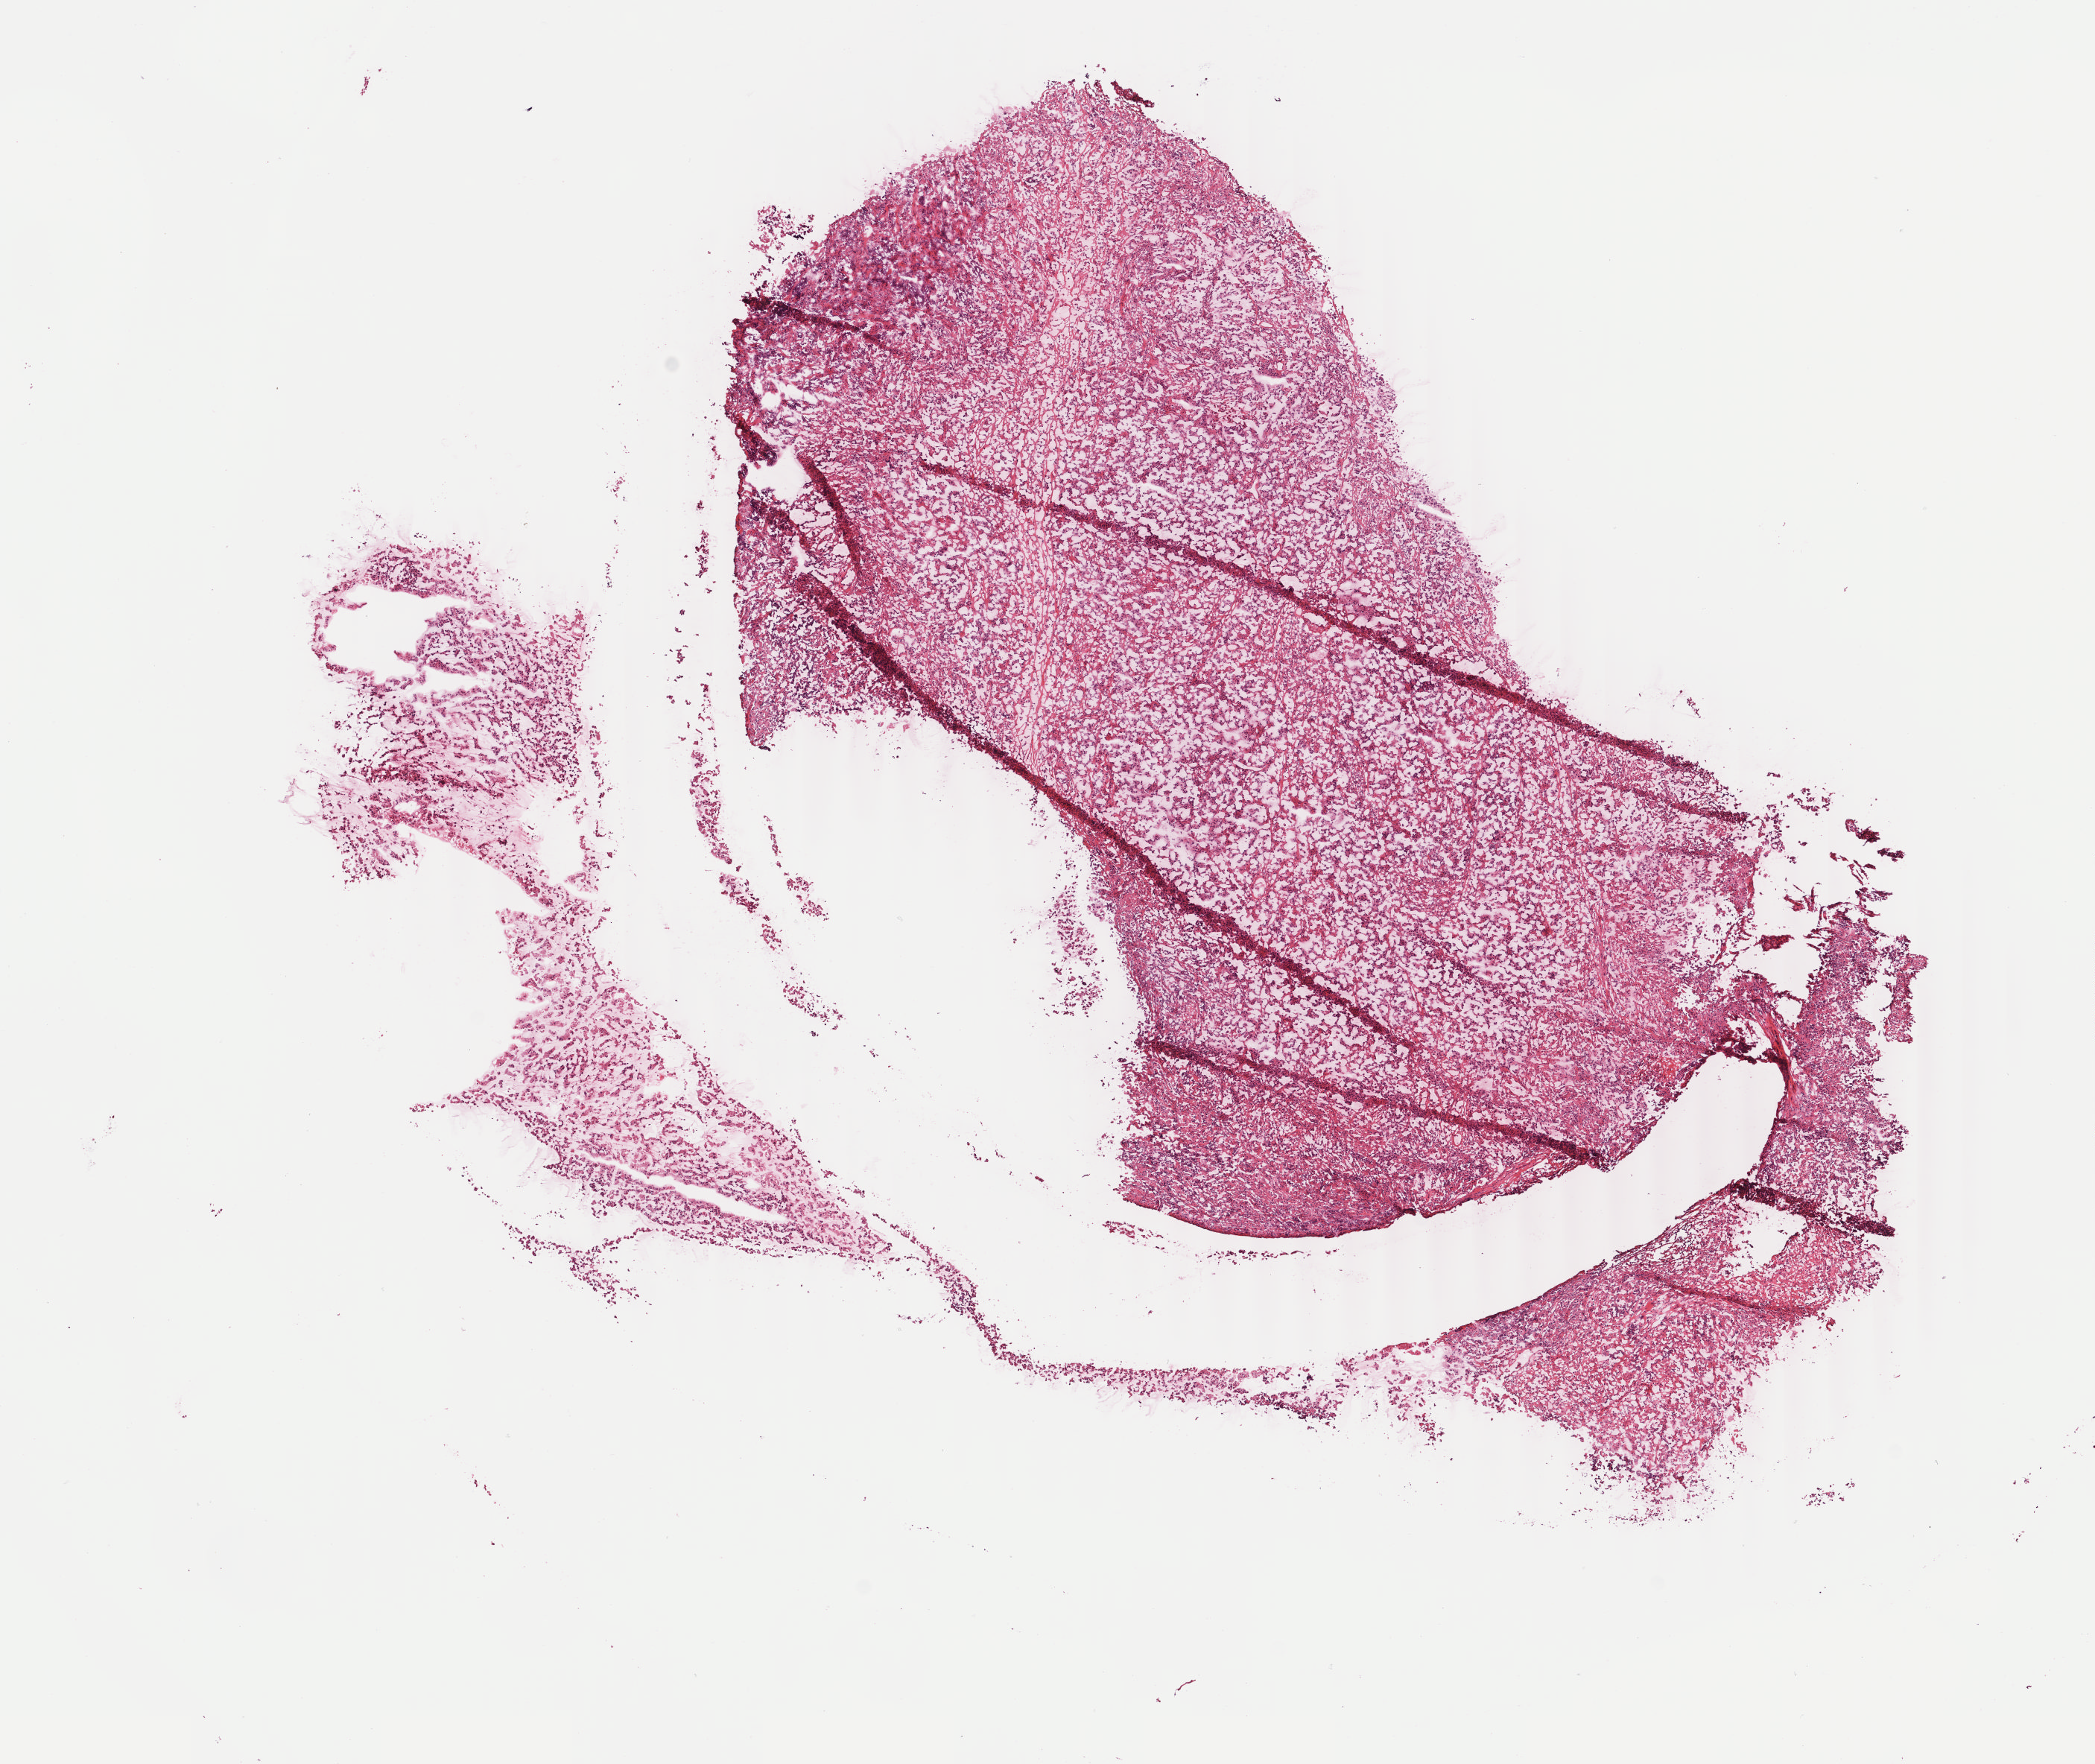
Digitized H&E tissue section (whole slide), whole scanned area (about 11.2 x 9.4 mm, from a 40x scan) shown as a low-resolution overview; frozen section from the top of the tissue portion; primary tumour sample from the testis. Male, age 50 years at initial diagnosis. Slide review estimates, as recorded: tumour cells 90%, tumour nuclei 90%, normal cells 0%, stromal cells 10%, necrosis 0%. Inflammatory infiltration, as recorded: lymphocyte infiltration 0%, monocyte infiltration 0%, neutrophil infiltration 0%.
- AJCC pathologic stage: IS (7th edition)
- TNM: T3 NX M0
- histologic diagnosis: Seminoma, NOS